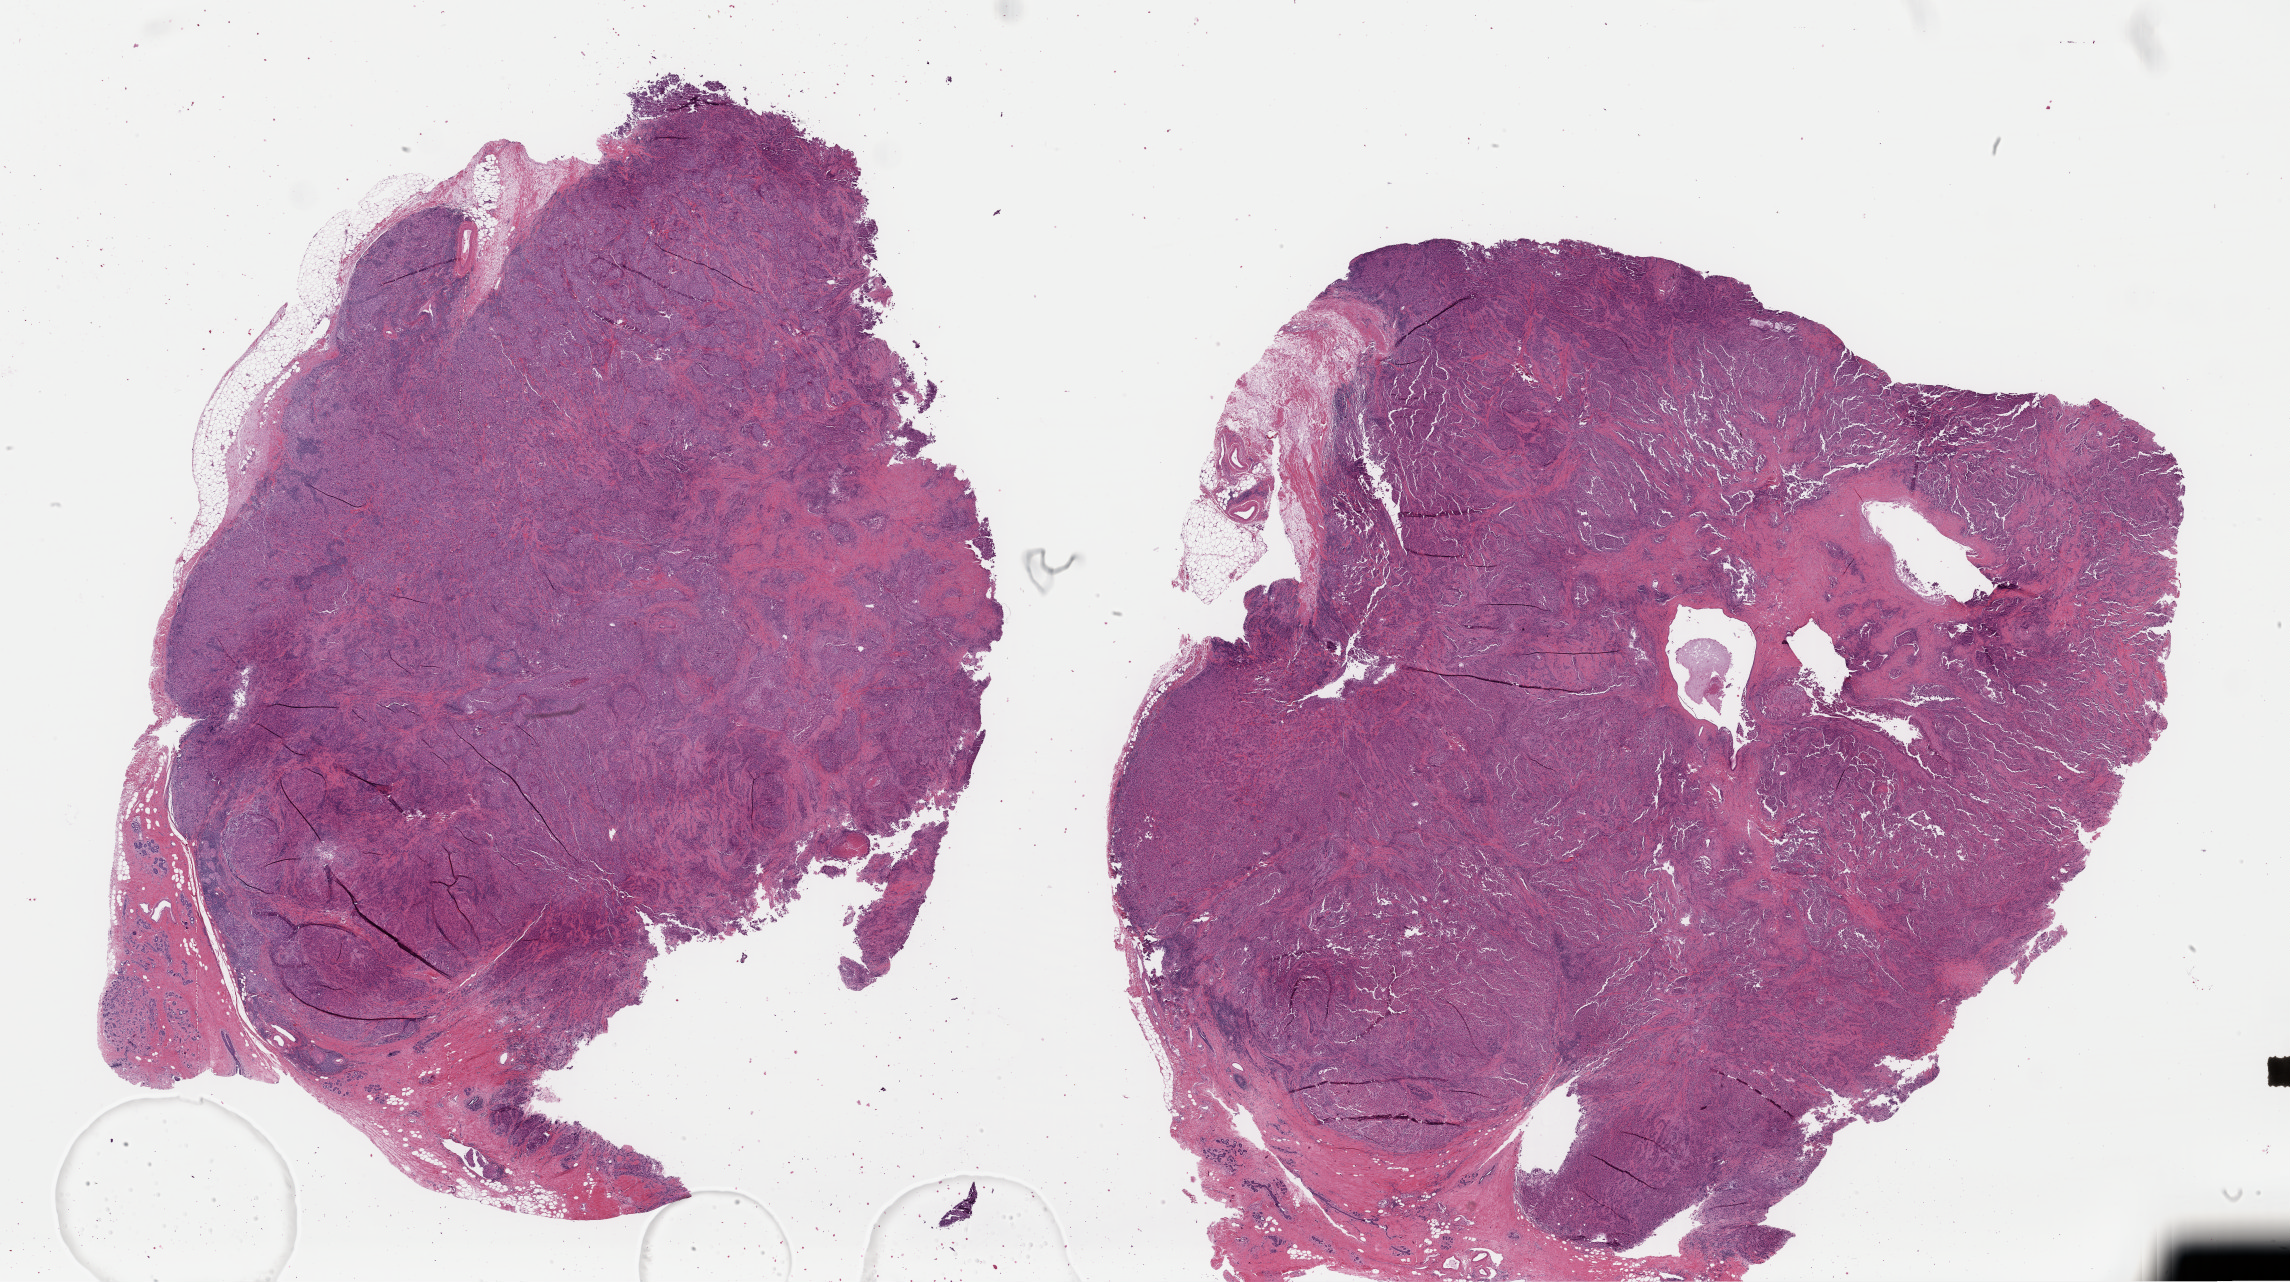
Hematoxylin and eosin (H&E) stained whole-slide image — shown as a low-resolution overview of the whole scanned area (about 36.2 x 20.3 mm). FFPE section. Primary tumour sample from the breast. Patient: female, age at initial diagnosis 50 years.
• lymph nodes positive (case pathology): 3 of 27 examined
• pathologic diagnosis: Infiltrating duct carcinoma, NOS
• AJCC pathologic stage: IIIA
• laterality: right
• TNM: T3 N1 M0